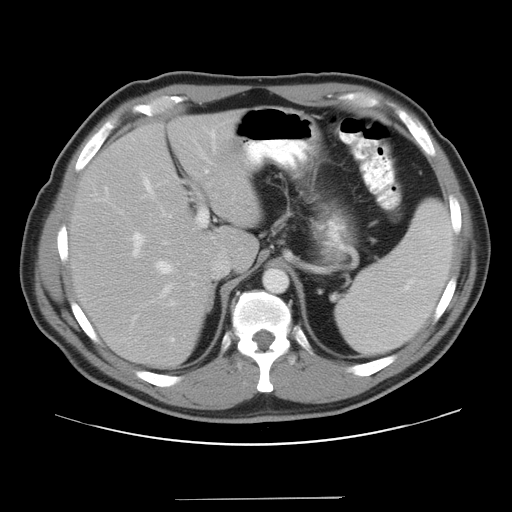
Contrast-enhanced abdominal CT, one axial slice; slice 28 of 37 in the series (ordered by position); 120 kVp; intravenous contrast given; soft-tissue window (W 400 / L 40 HU); 7.5 mm slice thickness; 512 × 512 image matrix, field of view 400 × 400 mm. Male patient, age 46 years. Case-level facts recorded for this patient, not image findings: diagnosis: colorectal cancer liver metastases, imaged before liver resection; multiple liver metastases: yes; largest metastasis: 1 cm.
Outlined on this slice (manually delineated by an expert):
- hepatic veins: bounding box <144,134,214,293> (left, top, right, bottom; pixels)
- liver: <71,114,258,367>
- planned liver remnant (the part of the liver to remain after resection): <71,114,258,367>
- portal vein (with intrahepatic branches): <131,148,212,342>